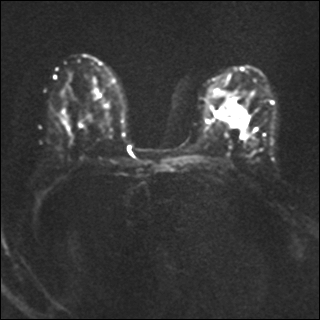
Breast MRI, one axial slice. Position 23 of 40 along the scan axis. Diffusion-weighted series; image 2 of 4 stored at this slice position (different b-values; order by instance number). 1.5 T. 4 mm slice thickness. 320 × 320 image matrix, field of view 320 × 320 mm. Female patient.
Outlined on this slice (expert manual segmentation):
- tumour on diffusion-weighted imaging: bounding box [x1, y1, x2, y2] px = [231, 104, 243, 126]